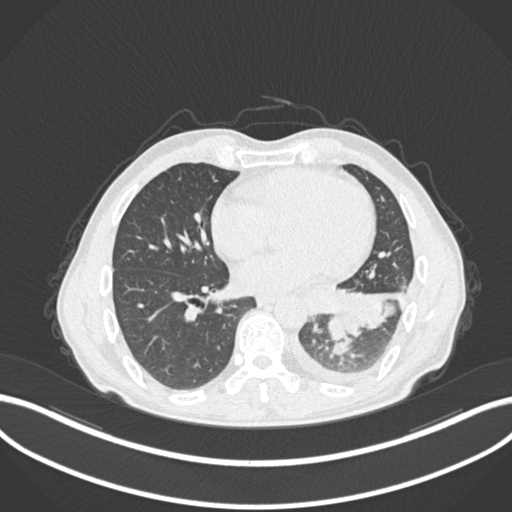
Chest CT, one axial slice. Slice 97 of 222 in the series (ordered by position). 120 kVp. Lung window (W 1500 / L -600 HU). 1 mm slice thickness. 512 × 512 image matrix, field of view 400 × 400 mm. Male patient, age 47 years. From the clinical record (not read from this slice): clinical TNM (as recorded): T3 N1 M1c; histopathological grade: G3.
Outlined on this slice (bounding box drawn by a radiologist):
- lung tumour (recorded histology: small cell carcinoma): bounding box [x1, y1, x2, y2] px = [322, 308, 363, 343]